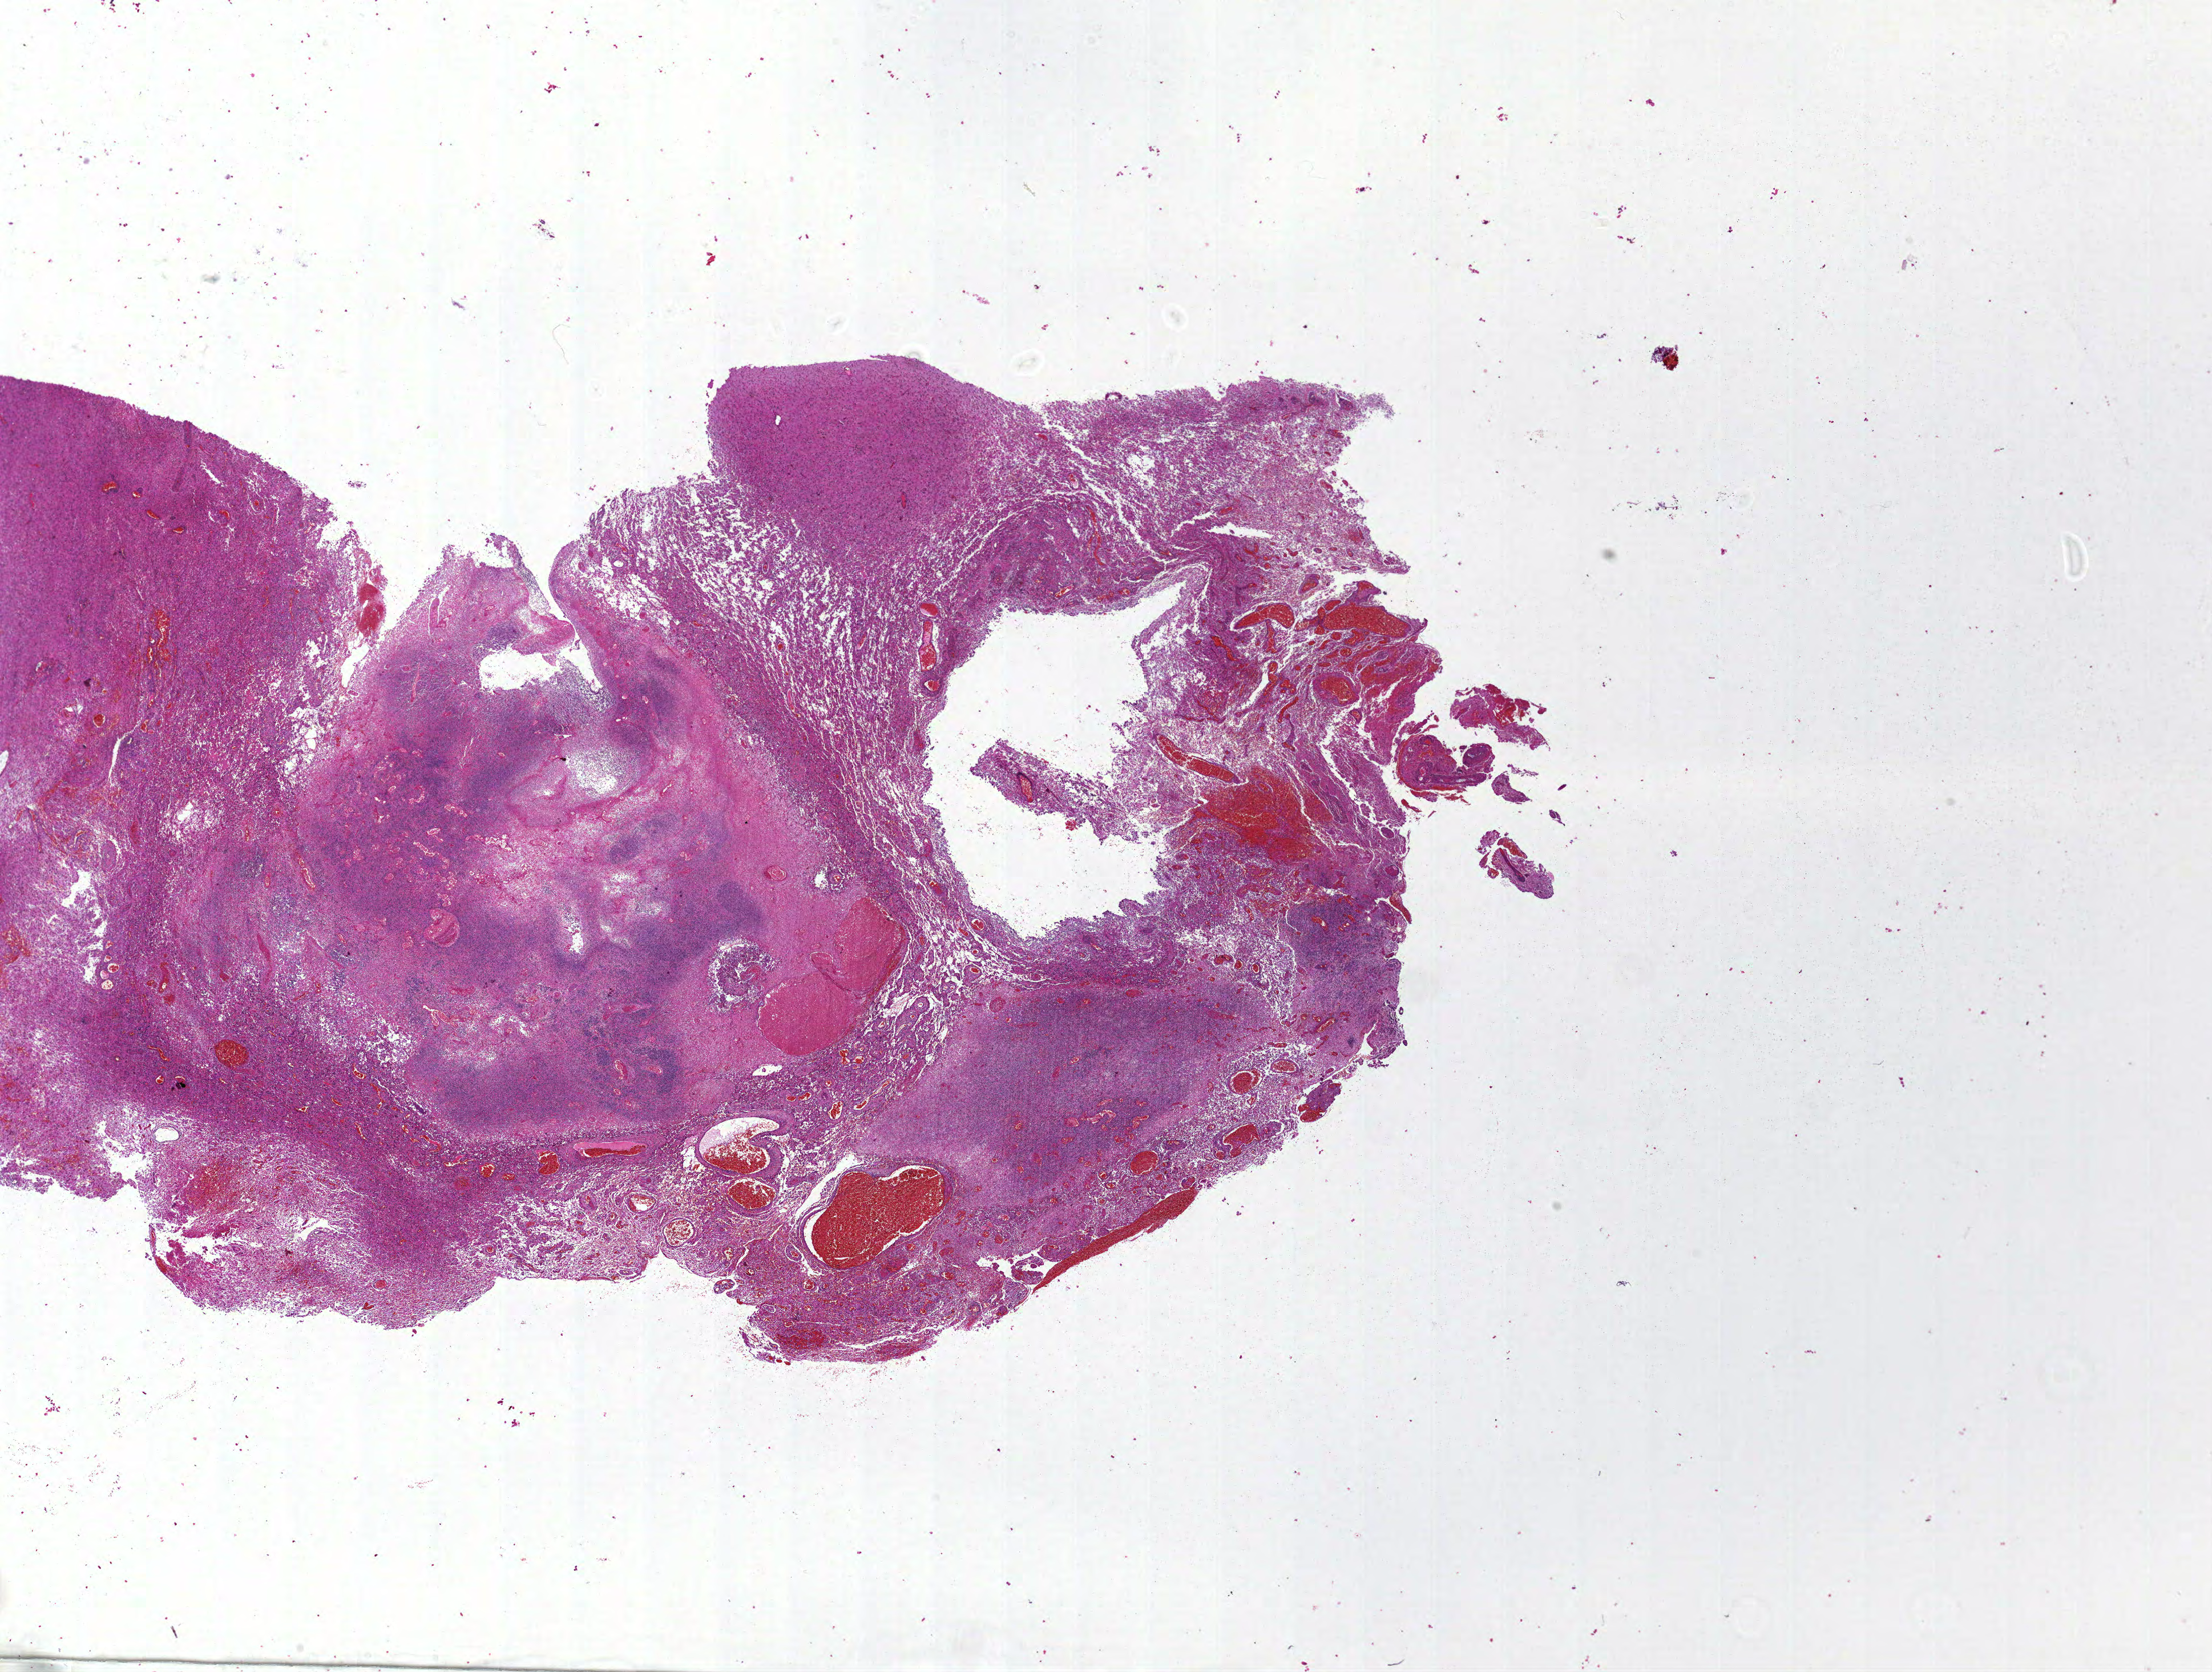
Digitized Hematoxylin and eosin (H&E) stained tissue section (whole slide), low-resolution overview of the scanned area, about 31.0 x 23.4 mm (from a 20x scan); formalin-fixed paraffin-embedded (FFPE) diagnostic section; sample: primary tumour, brain. Male patient; age at initial diagnosis 62 years.
Pathologic diagnosis: Glioblastoma.